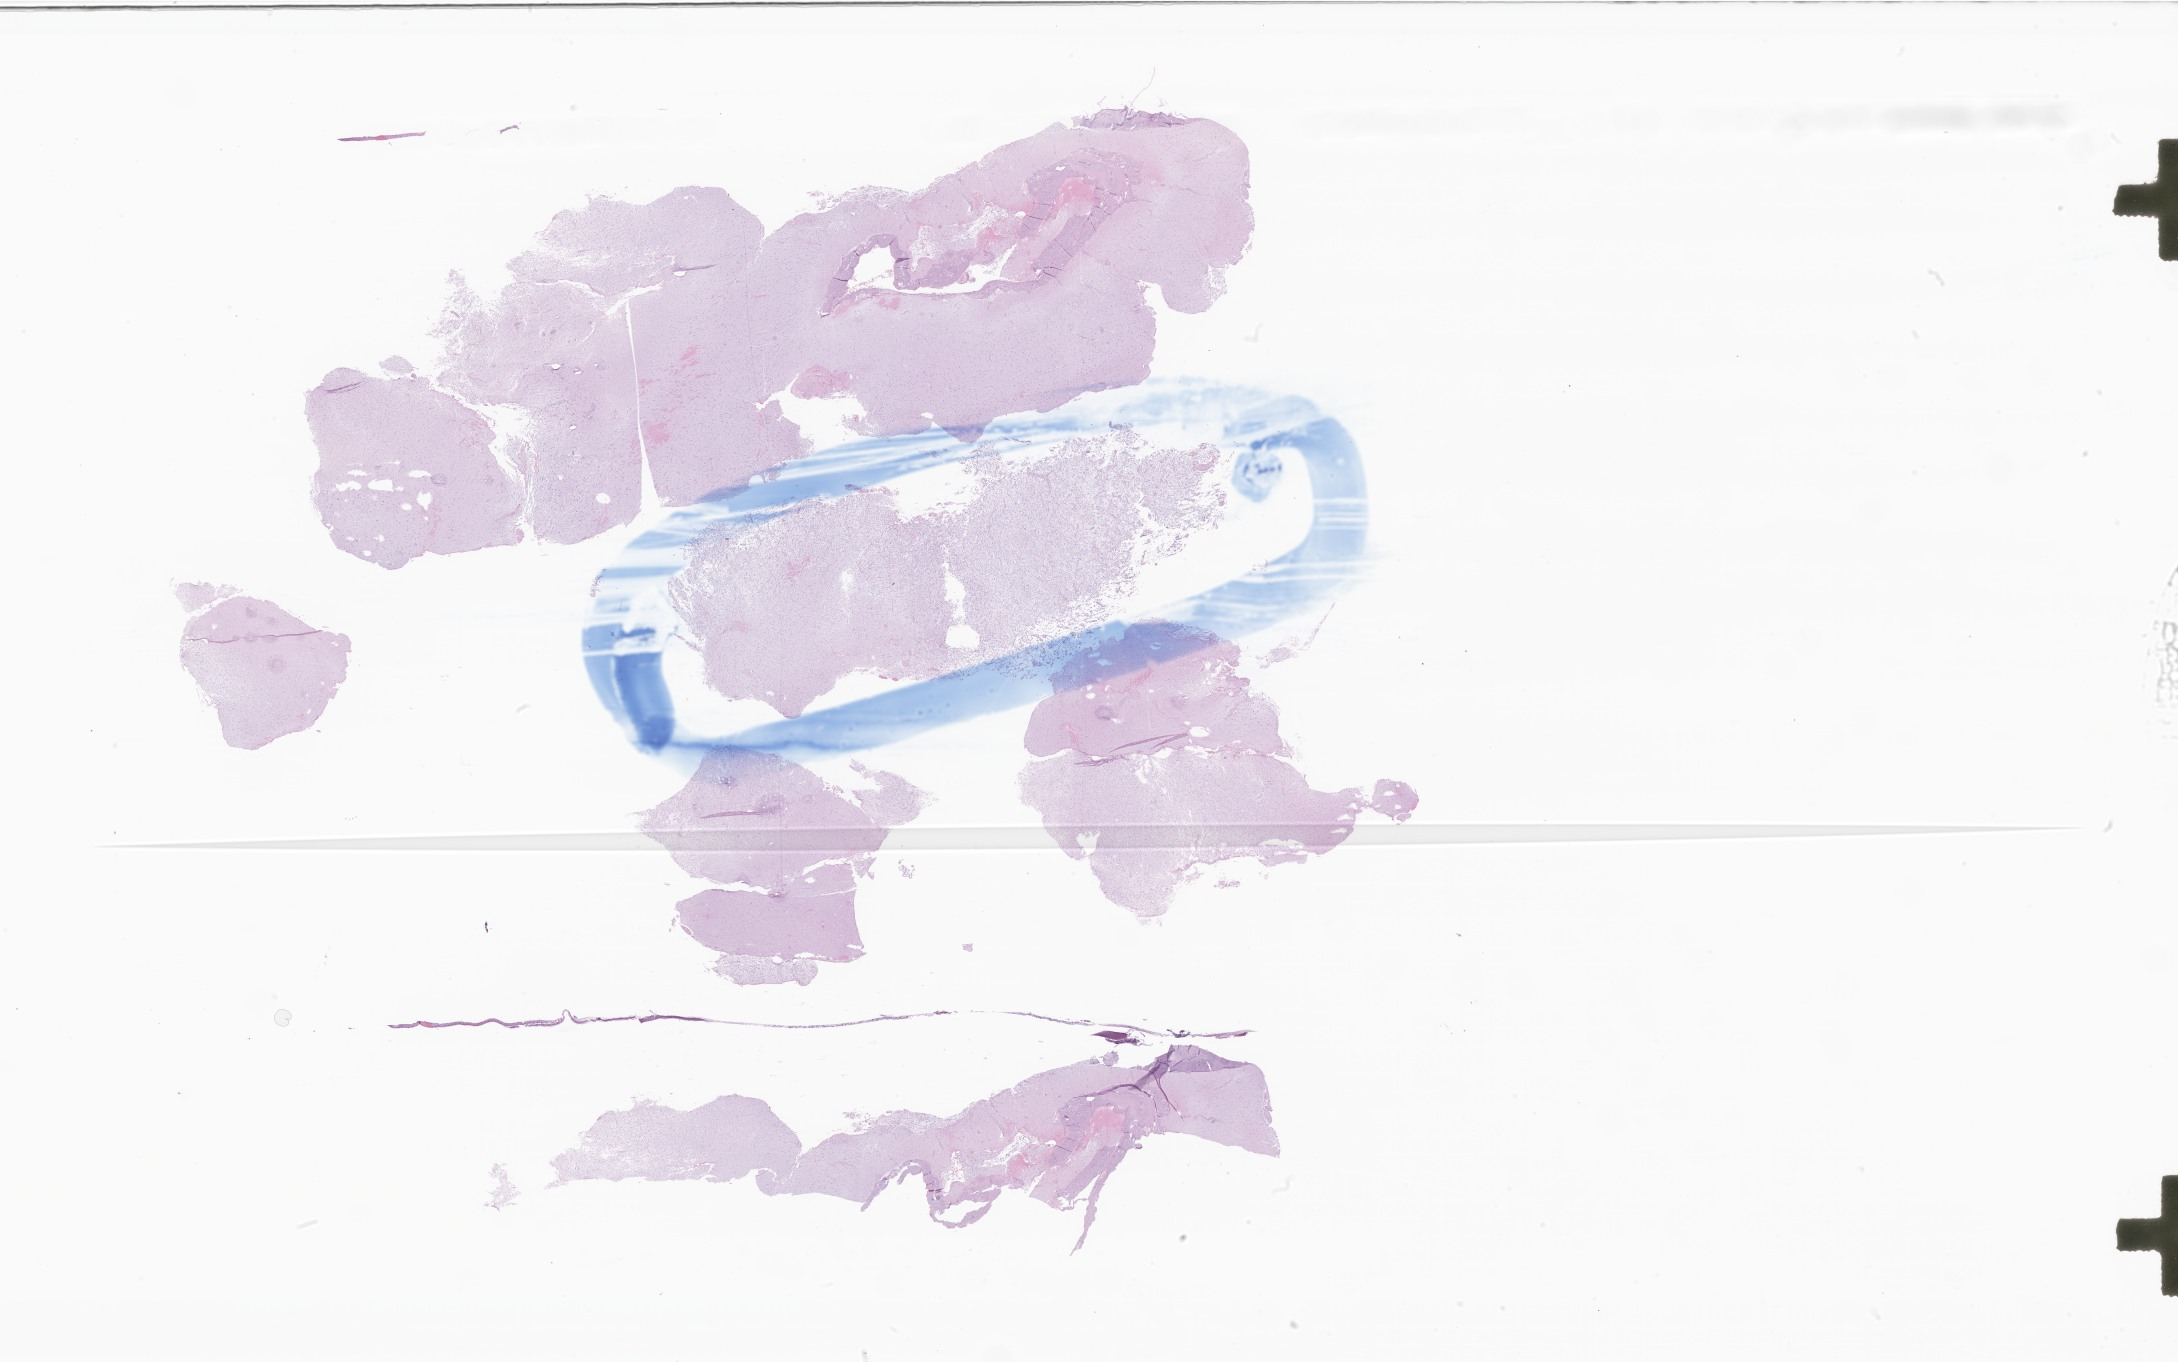
Whole-slide image, haematoxylin and eosin stain of tumor tissue from the brain, shown as a low-resolution overview of the whole scanned area (about 36.7 x 23.0 mm). Male patient, age 203 months.
Specimen: formalin-fixed paraffin-embedded section.